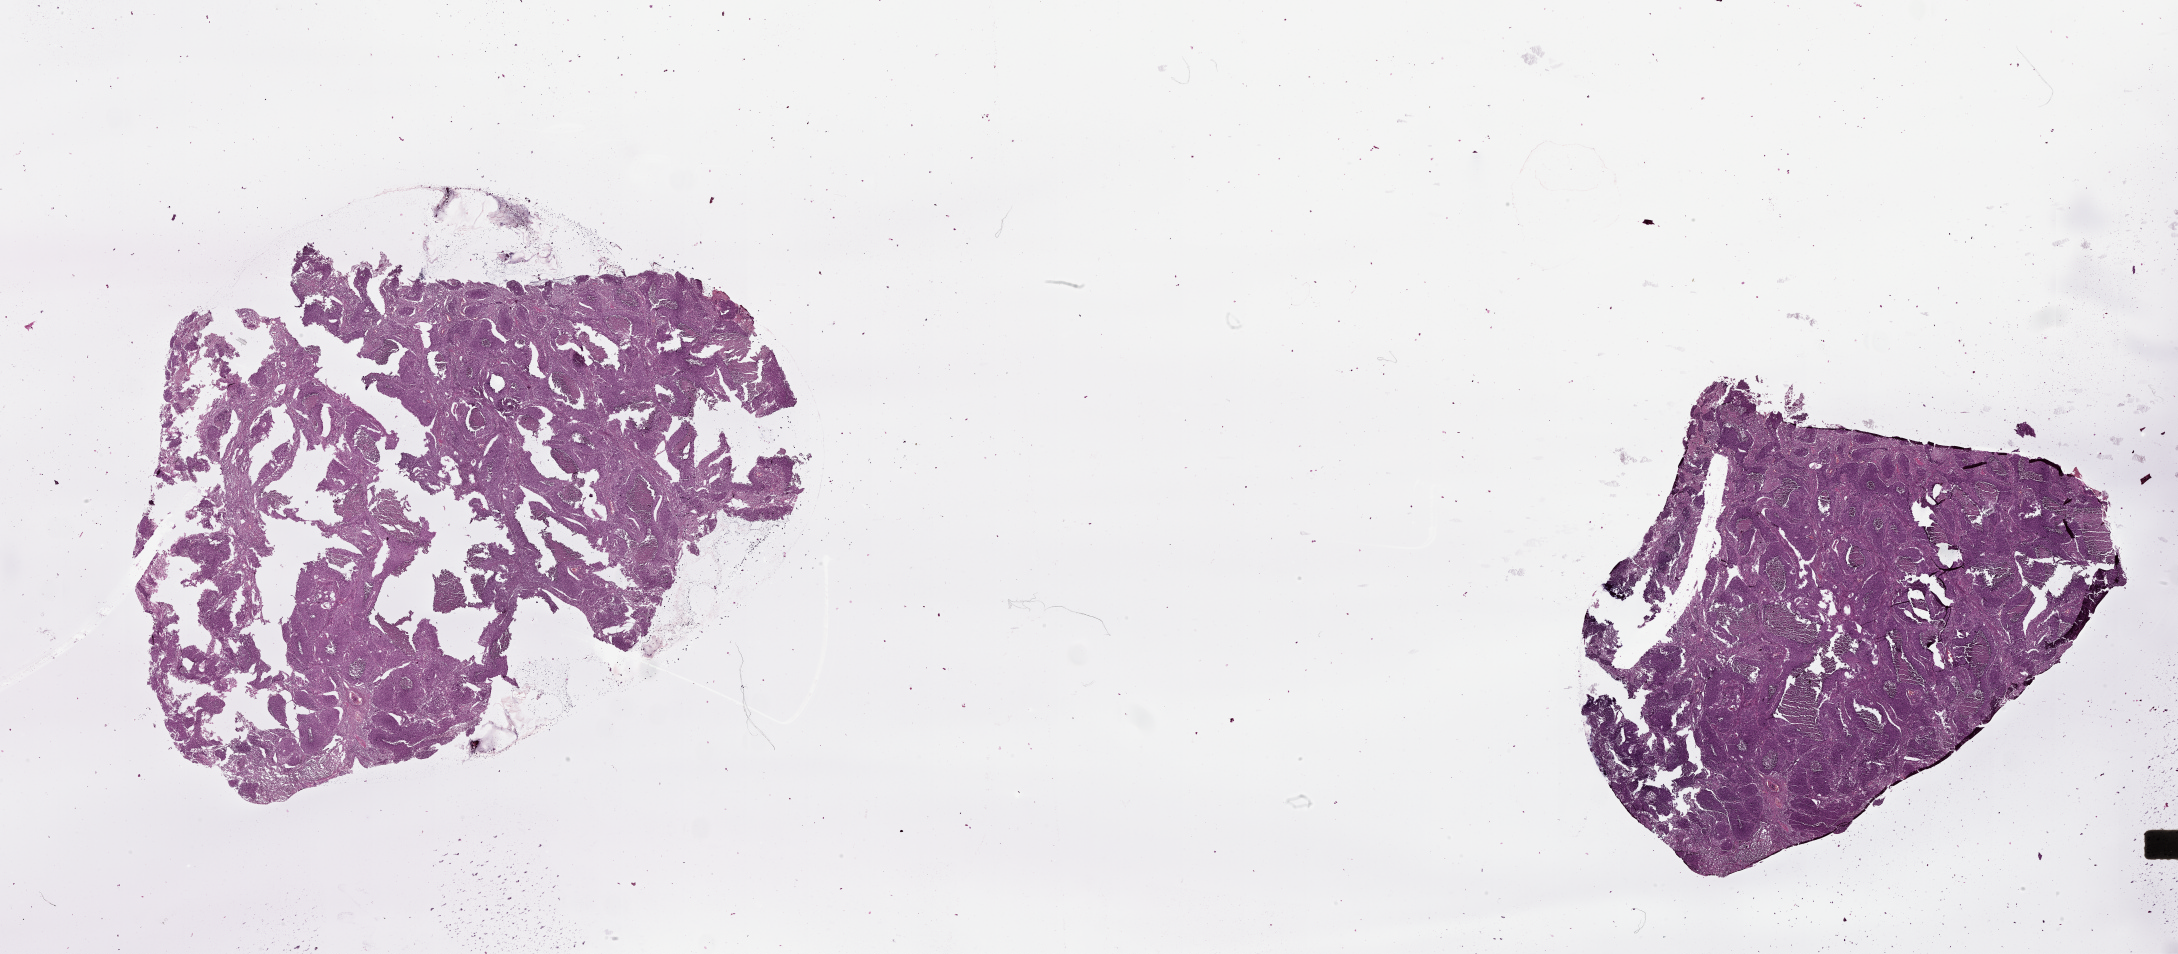
Digitized H&E tissue section (whole slide) — low-resolution overview of the scanned area, about 35.1 x 15.4 mm (from a 20x scan), lung, tumour tissue. Patient: male, age 68 years.
* patient diagnosis (cohort enrolment): squamous cell carcinoma (lung)